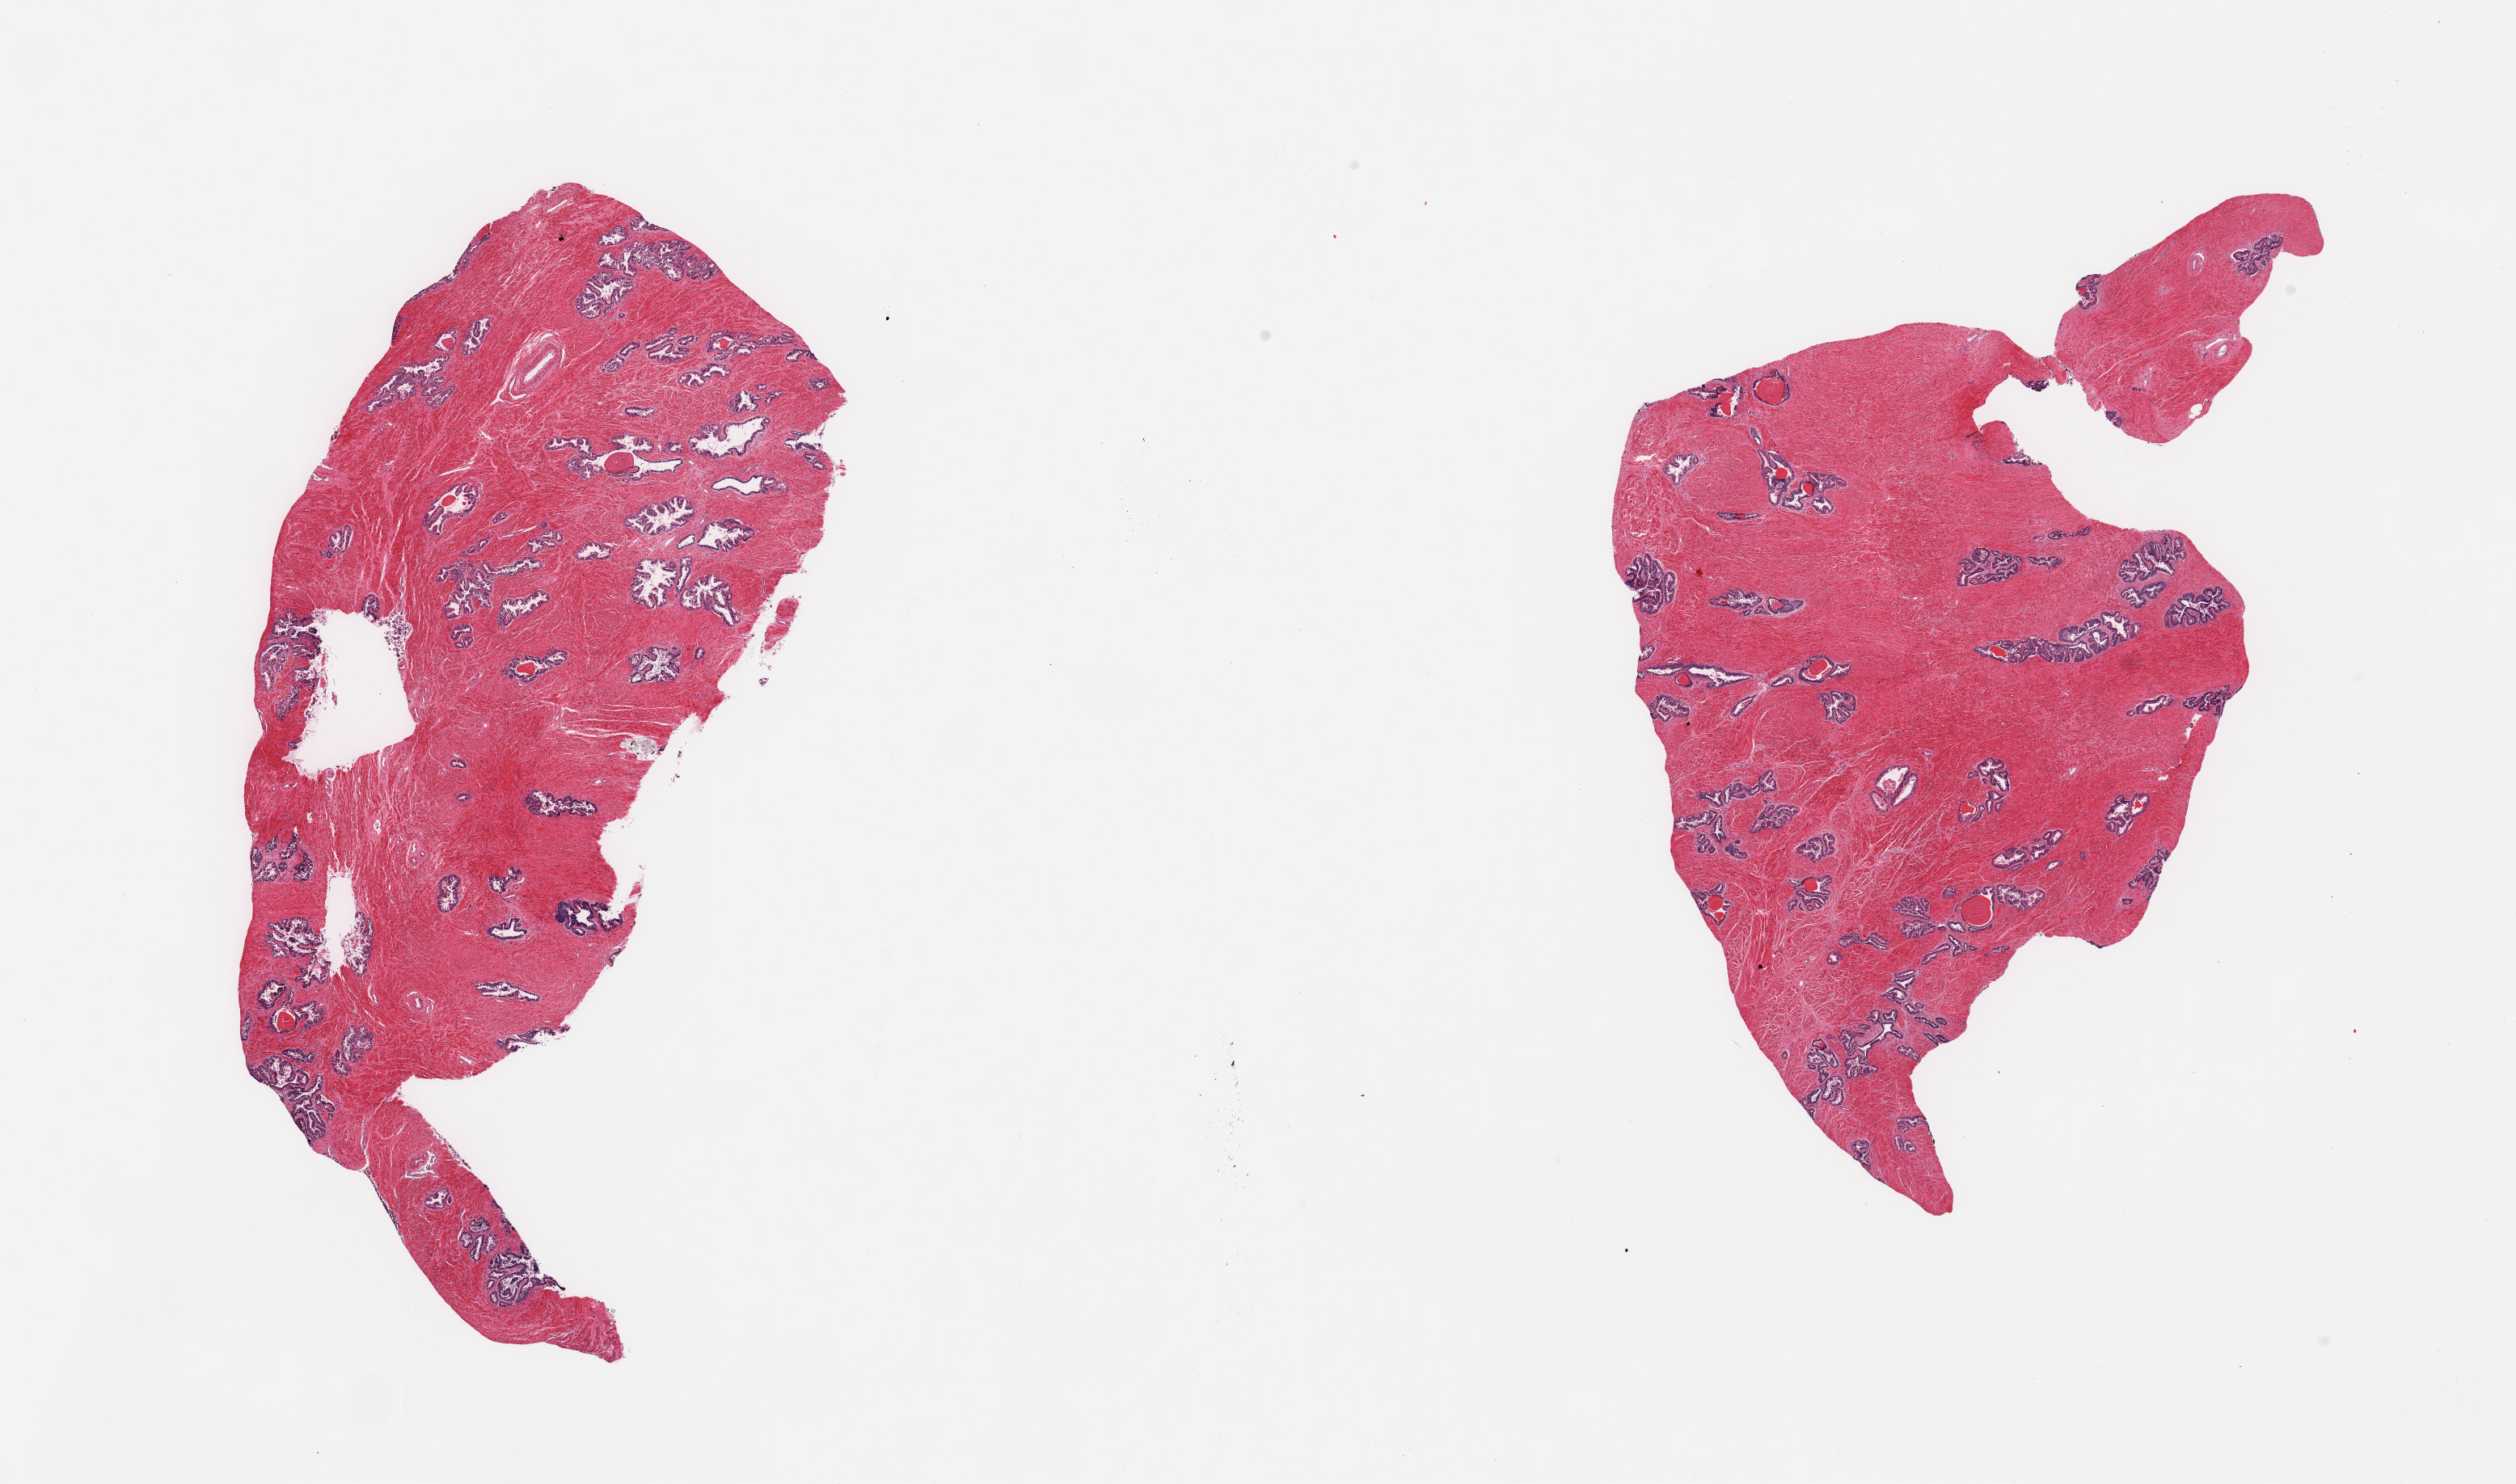
Hematoxylin and eosin (H&E) whole-slide image — shown as a low-resolution overview of the whole scanned area (about 24.6 x 14.5 mm); PAXgene-fixed, paraffin-embedded tissue; section of prostate (target tissue); donor tissue sample. Donor: male.
• review note (as recorded): 2 pieces; fibromuscular stroma and glandular structures